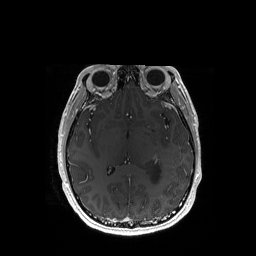
Brain MRI from a brain-tumour surgery series, one axial slice. Slice 91 of 192 in the series (ordered by position). T1-weighted post-contrast. 256 × 256 image matrix, field of view 256 × 256 mm. Case-level facts recorded for this patient, not image findings: histopathology: Astrocytoma; WHO grade: 3; IDH mutation: yes; tumour location: Left Temporal.
Structures marked on this image (expert manual segmentation):
- tumour: bounding box <150,161,162,183> (left, top, right, bottom; pixels)